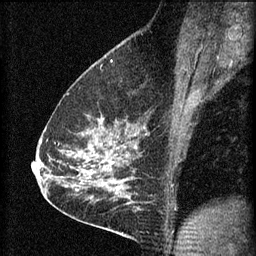
Breast MRI (dynamic contrast-enhanced), one sagittal slice; 3 images stored at this slice position (order not interpretable as contrast timing); 1.5 T; TE 4.2 ms, TR 8.2 ms; 2 mm slice thickness; 256 × 256 image matrix. Female patient, age 59 years.
Outlined on this slice (semi-automatic segmentation, software-assisted and operator-edited):
- analysis volume of interest (the breast-tissue region the enhancement analysis was run in; not a lesion): box from (x=61, y=104) to (x=134, y=161) px
- tumour enhancement mask (voxels above the 70 % enhancement threshold inside the analysis volume of interest): (x=89, y=142)–(x=115, y=151)